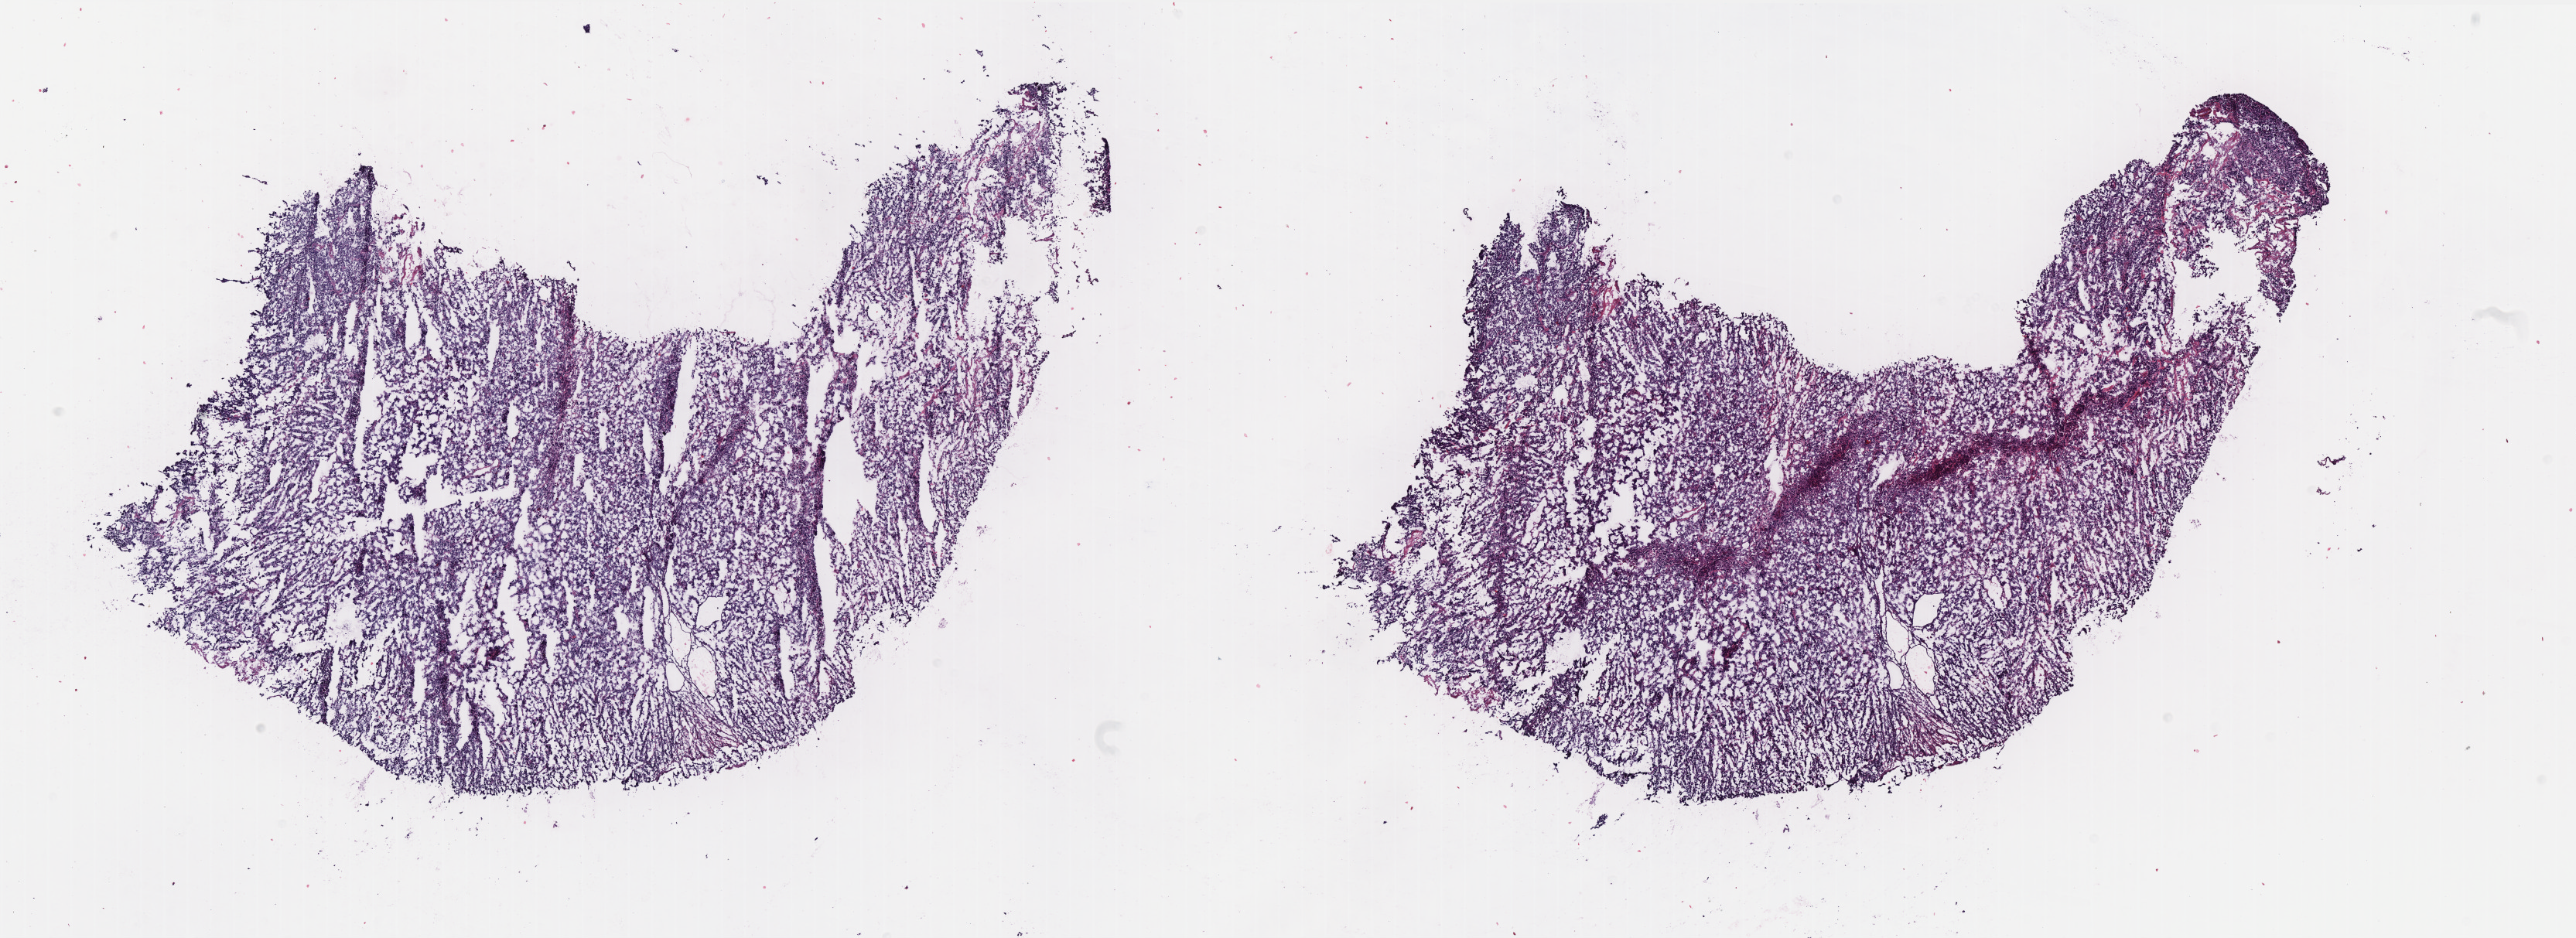
Whole-slide histology image, Hematoxylin and eosin (H&E) stained — shown as a low-resolution overview of the whole scanned area (about 26.7 x 9.7 mm); frozen section; primary tumour sample from the uterus. Female, age 71 years at initial diagnosis.
Histologic diagnosis: Serous cystadenocarcinoma, NOS.